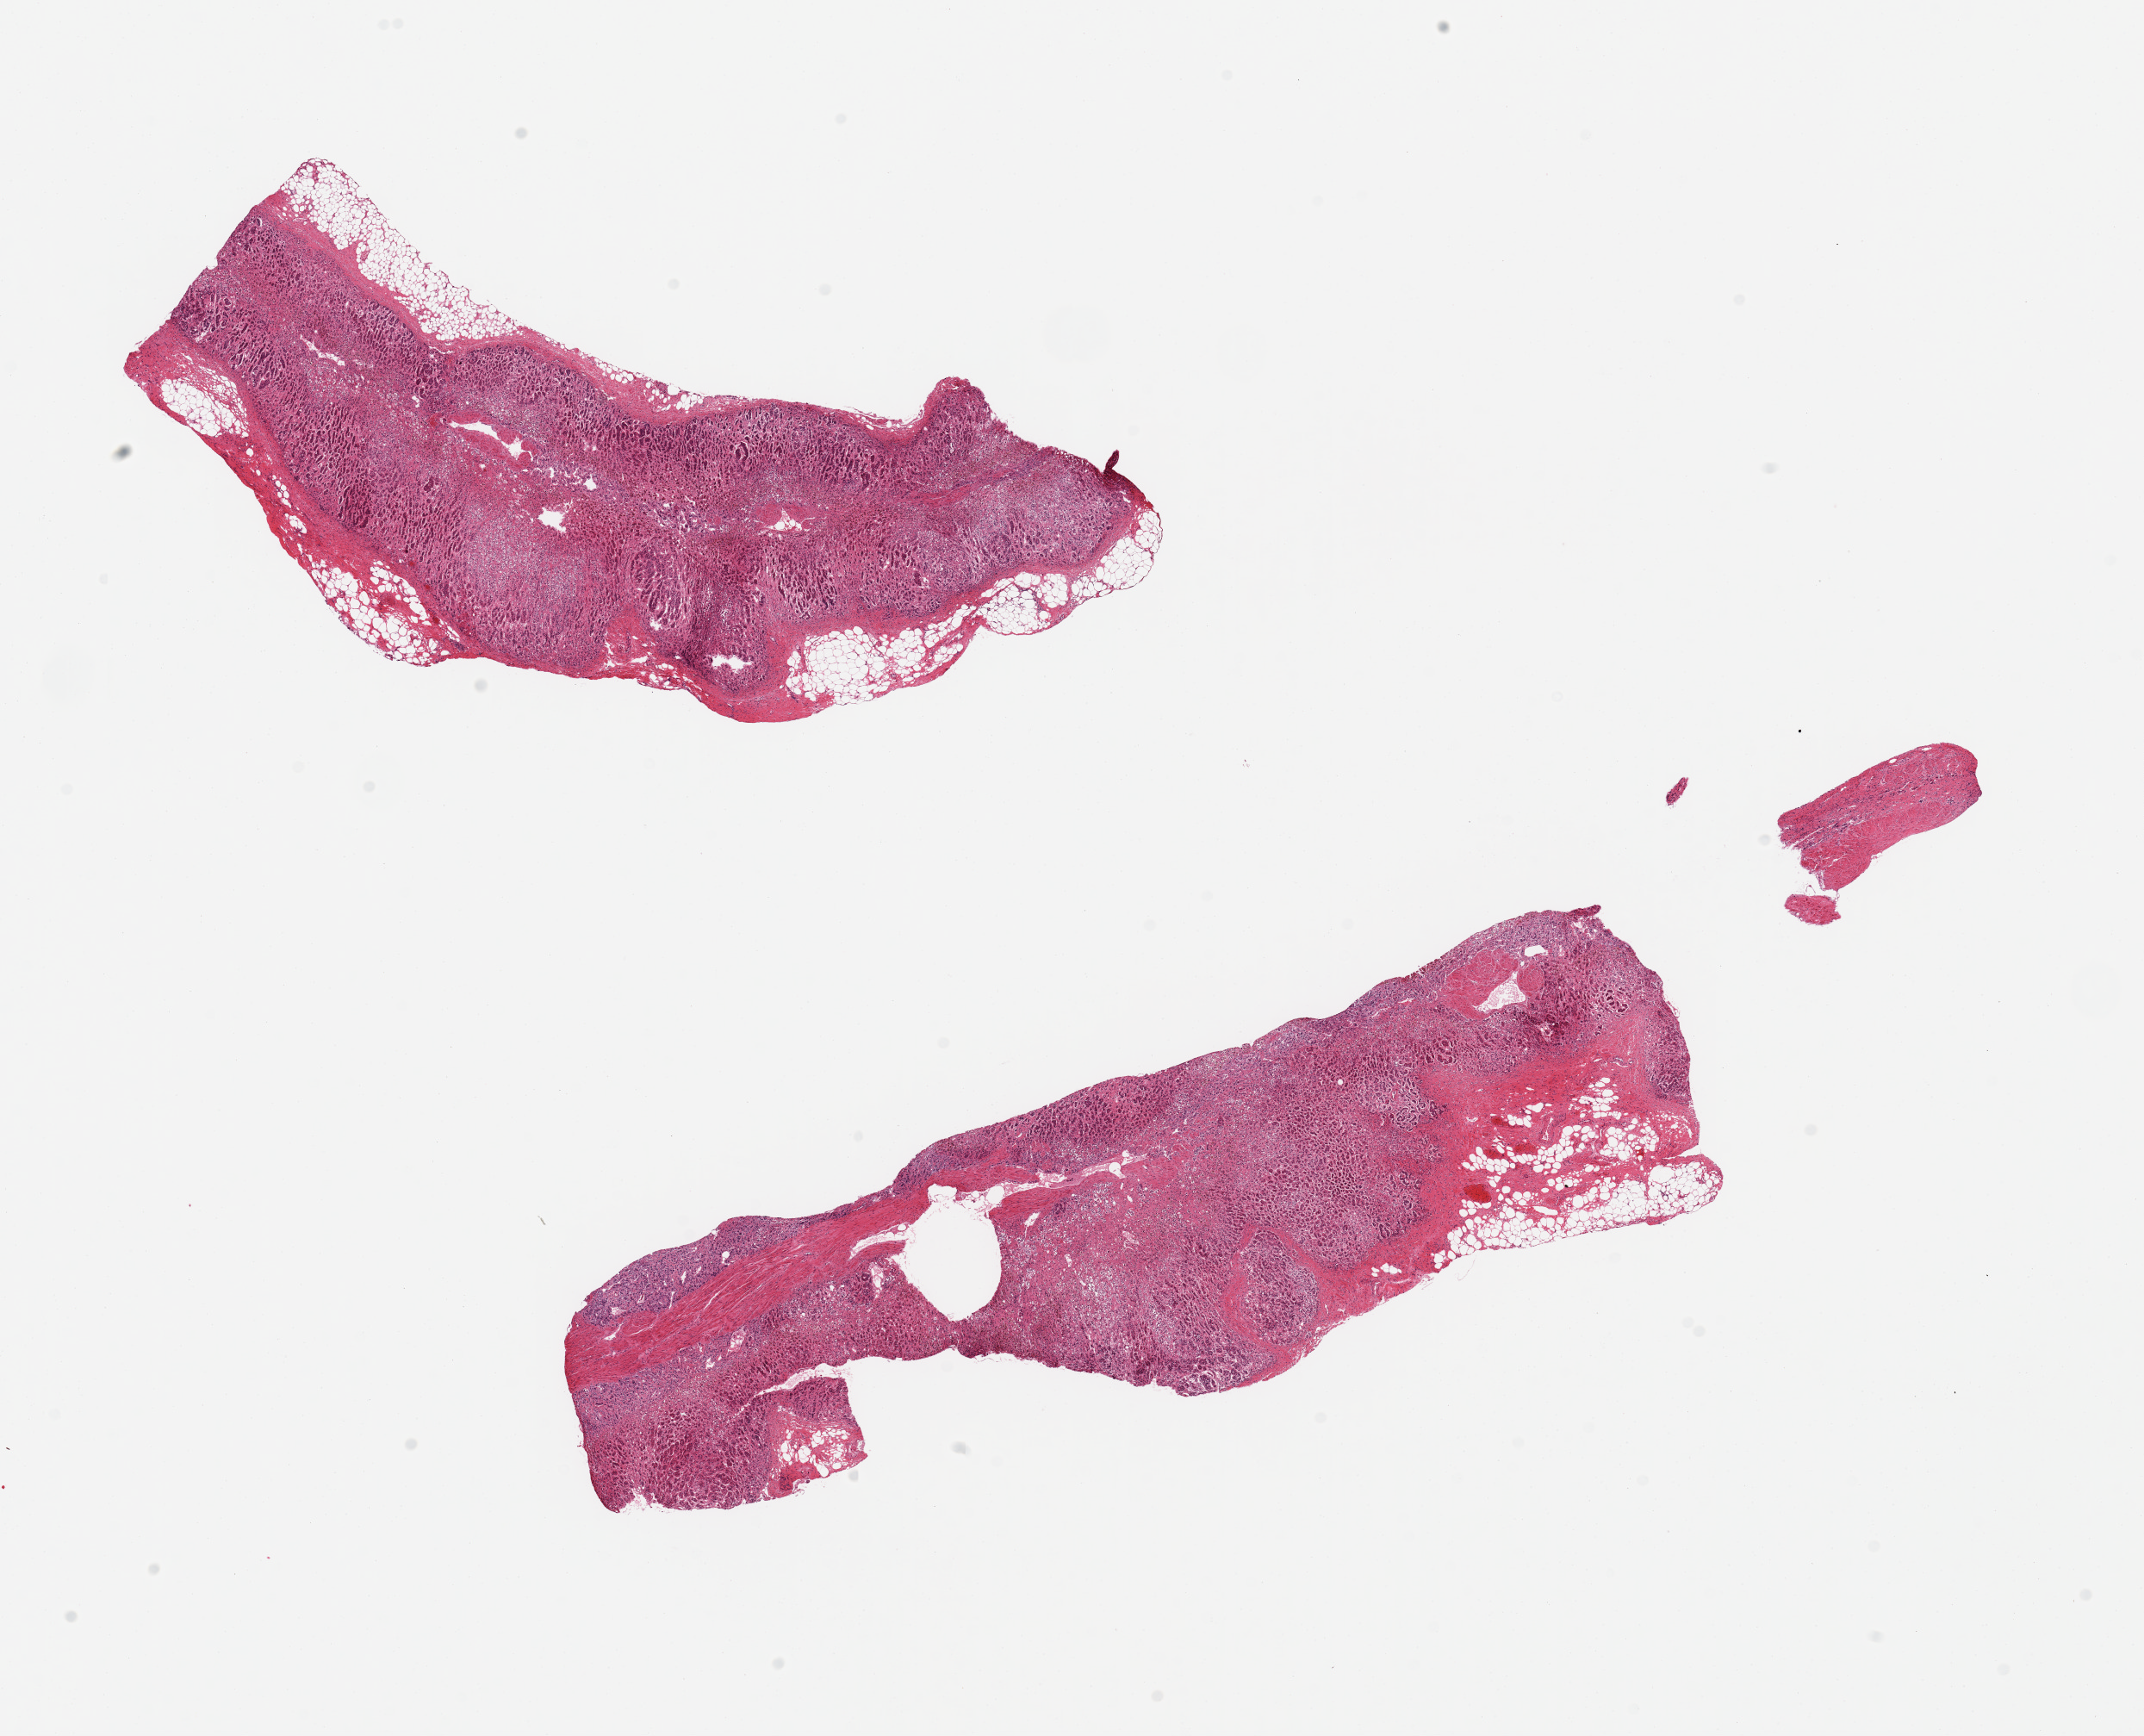
Digitized haematoxylin and eosin-stained section, whole scanned area (about 19.7 x 15.9 mm) shown as a low-resolution overview; PAXgene-fixed, paraffin-embedded tissue; target tissue: adrenal gland; donor tissue sample. Donor: male.
Reviewer comment on this tissue sample: 2 pieces; cortex and medulla, includes 10 and 20% attached fat.